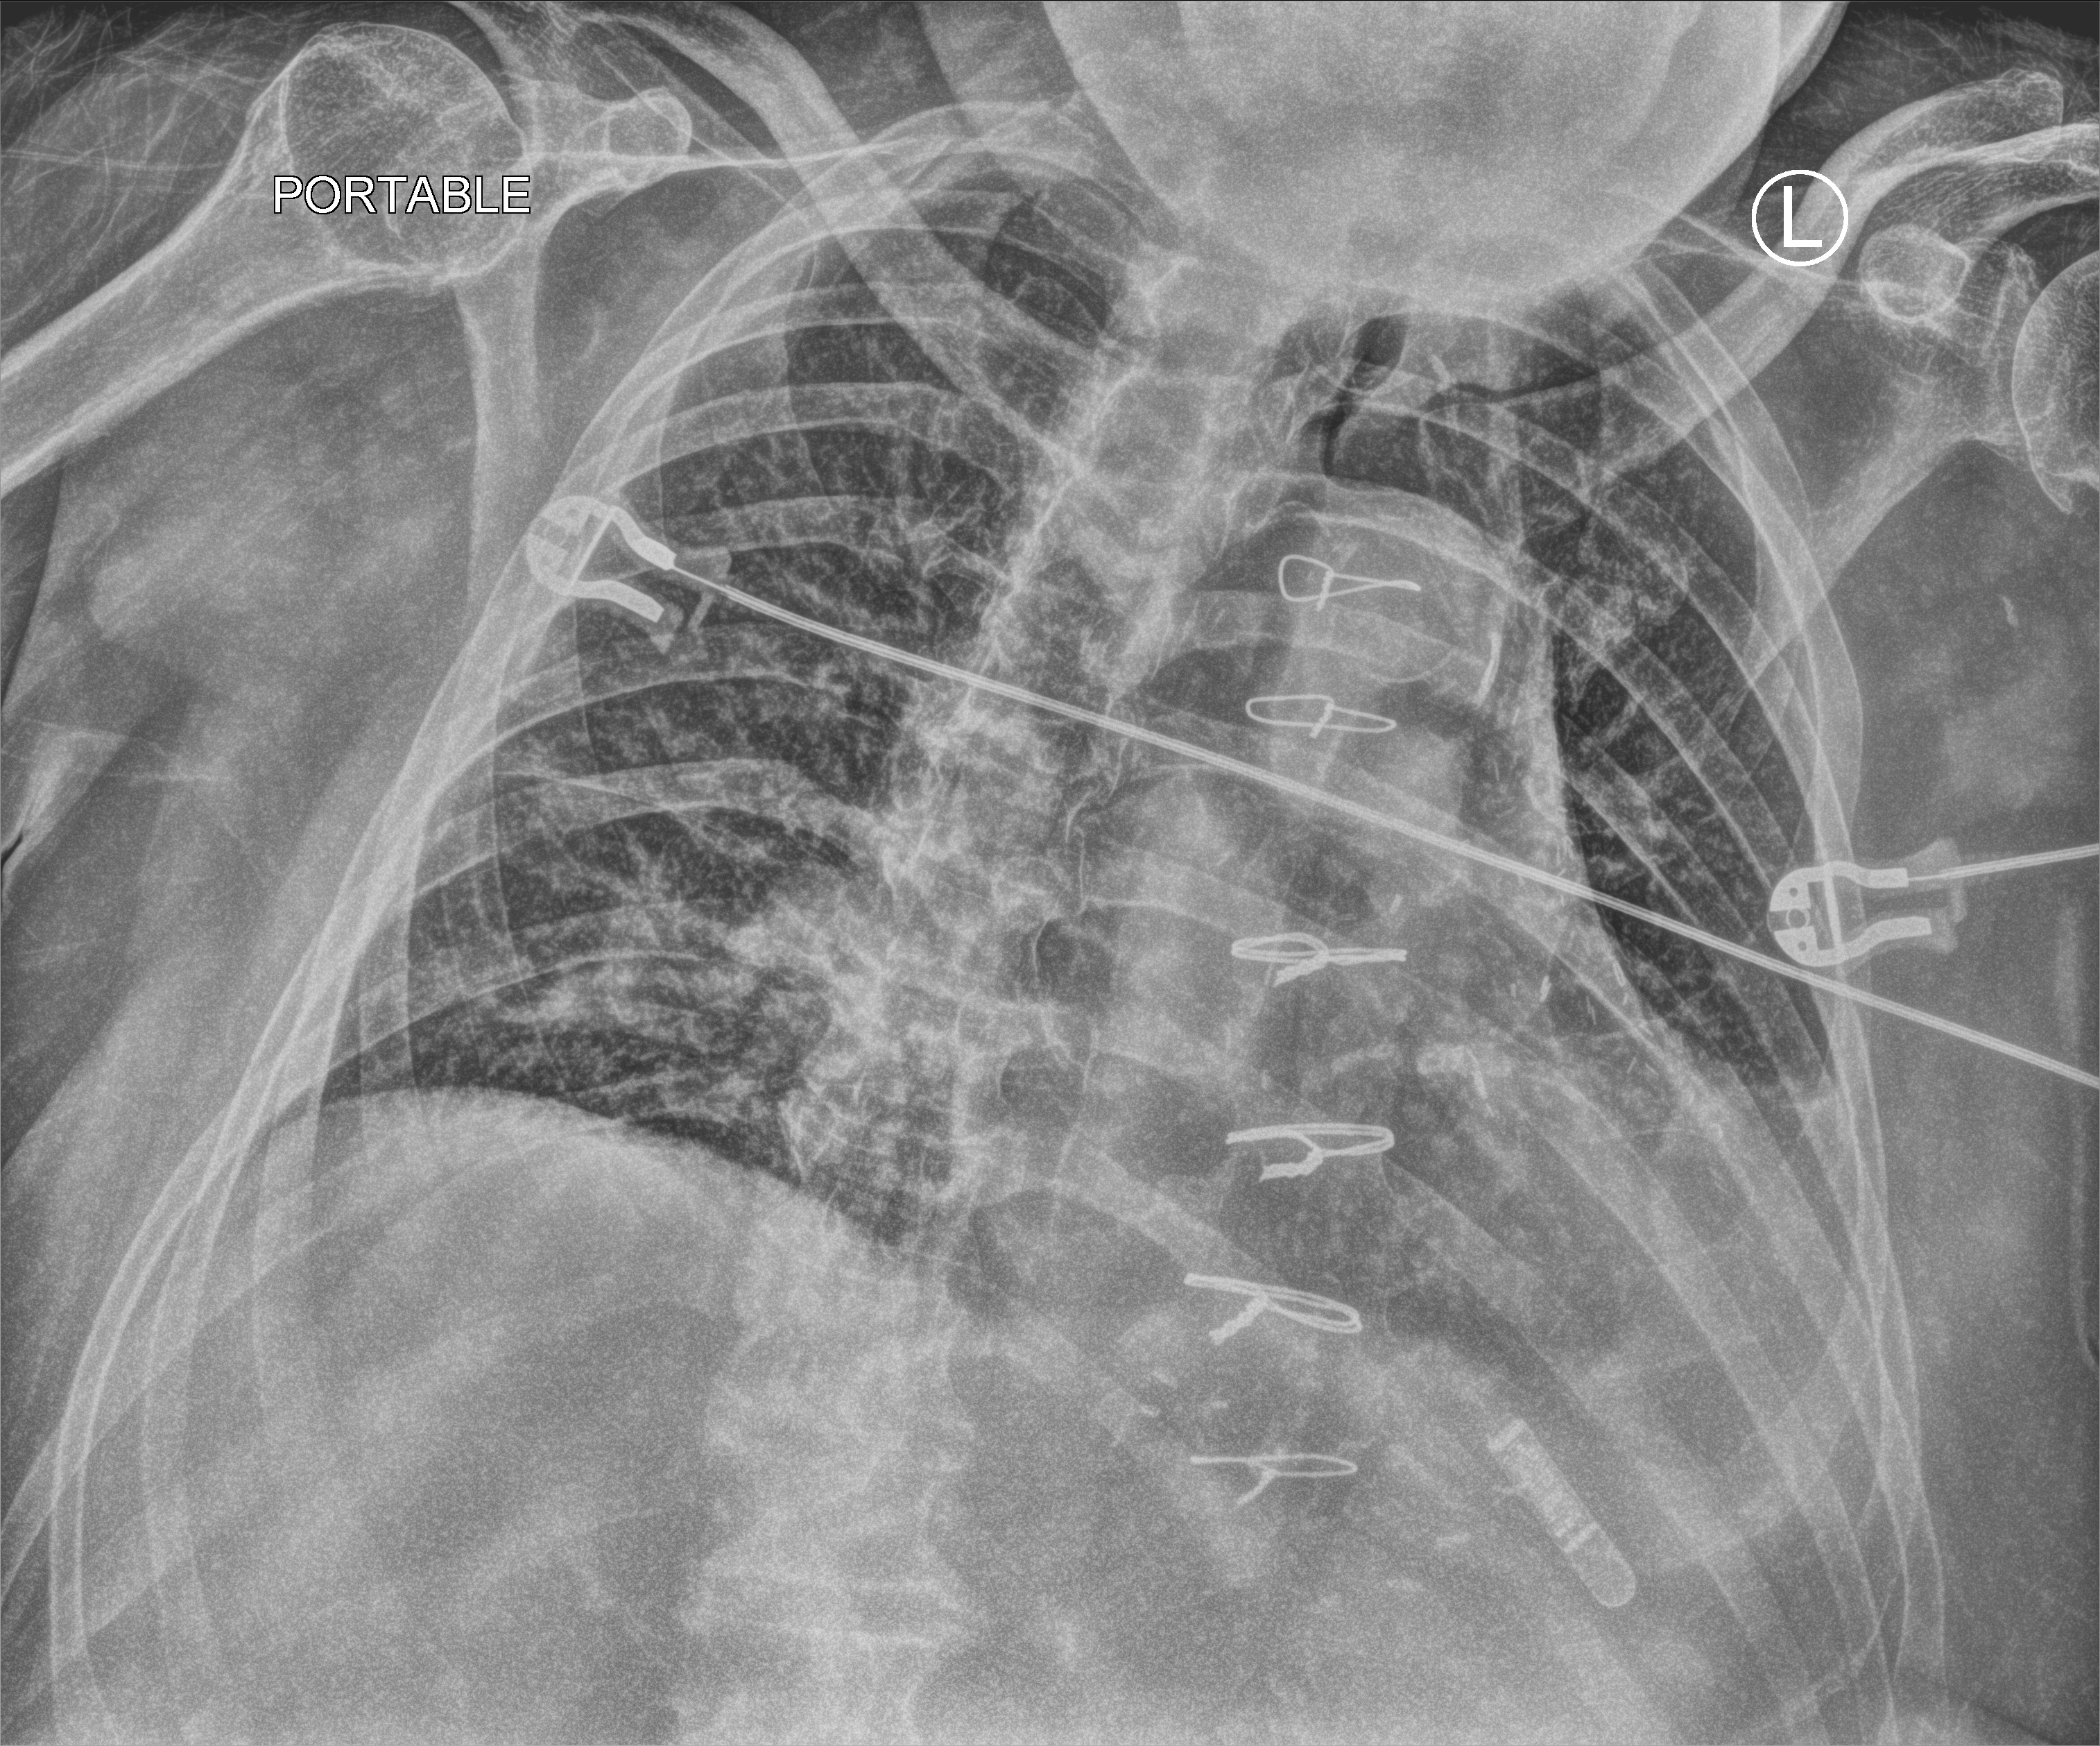
Portable chest radiograph, anteroposterior (AP) projection. Male patient hospitalised with COVID-19, age 60–74 years.
Admission-level facts for this patient (not findings on this image; timing relative to this image not recorded): smoking status (admission record): never; mechanically ventilated during this hospital stay: no; chronic kidney disease (admission record): yes.